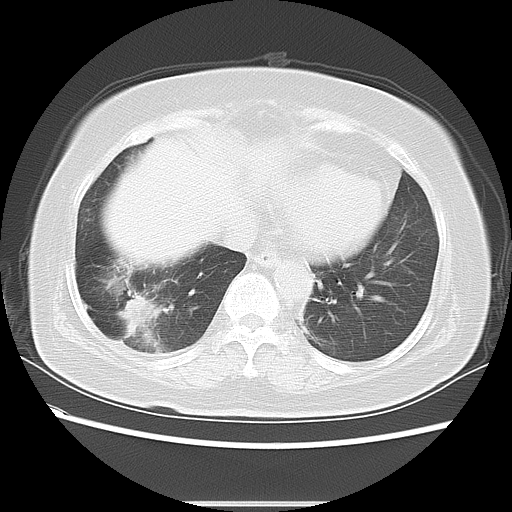
Chest CT, one axial slice; position 20 of 61 along the scan axis; lung window (W 1500 / L -600 HU); 5 mm slice thickness; 512 × 512 image matrix, field of view 350 × 350 mm. Female patient, age 65 years. Case-level facts recorded for this patient, not image findings: clinical TNM (as recorded): T2 N0 M1b.
Outlined on this slice (bounding box drawn by a radiologist):
- lung tumour (recorded histology: adenocarcinoma): bounding box <119,293,148,339> (left, top, right, bottom; pixels)